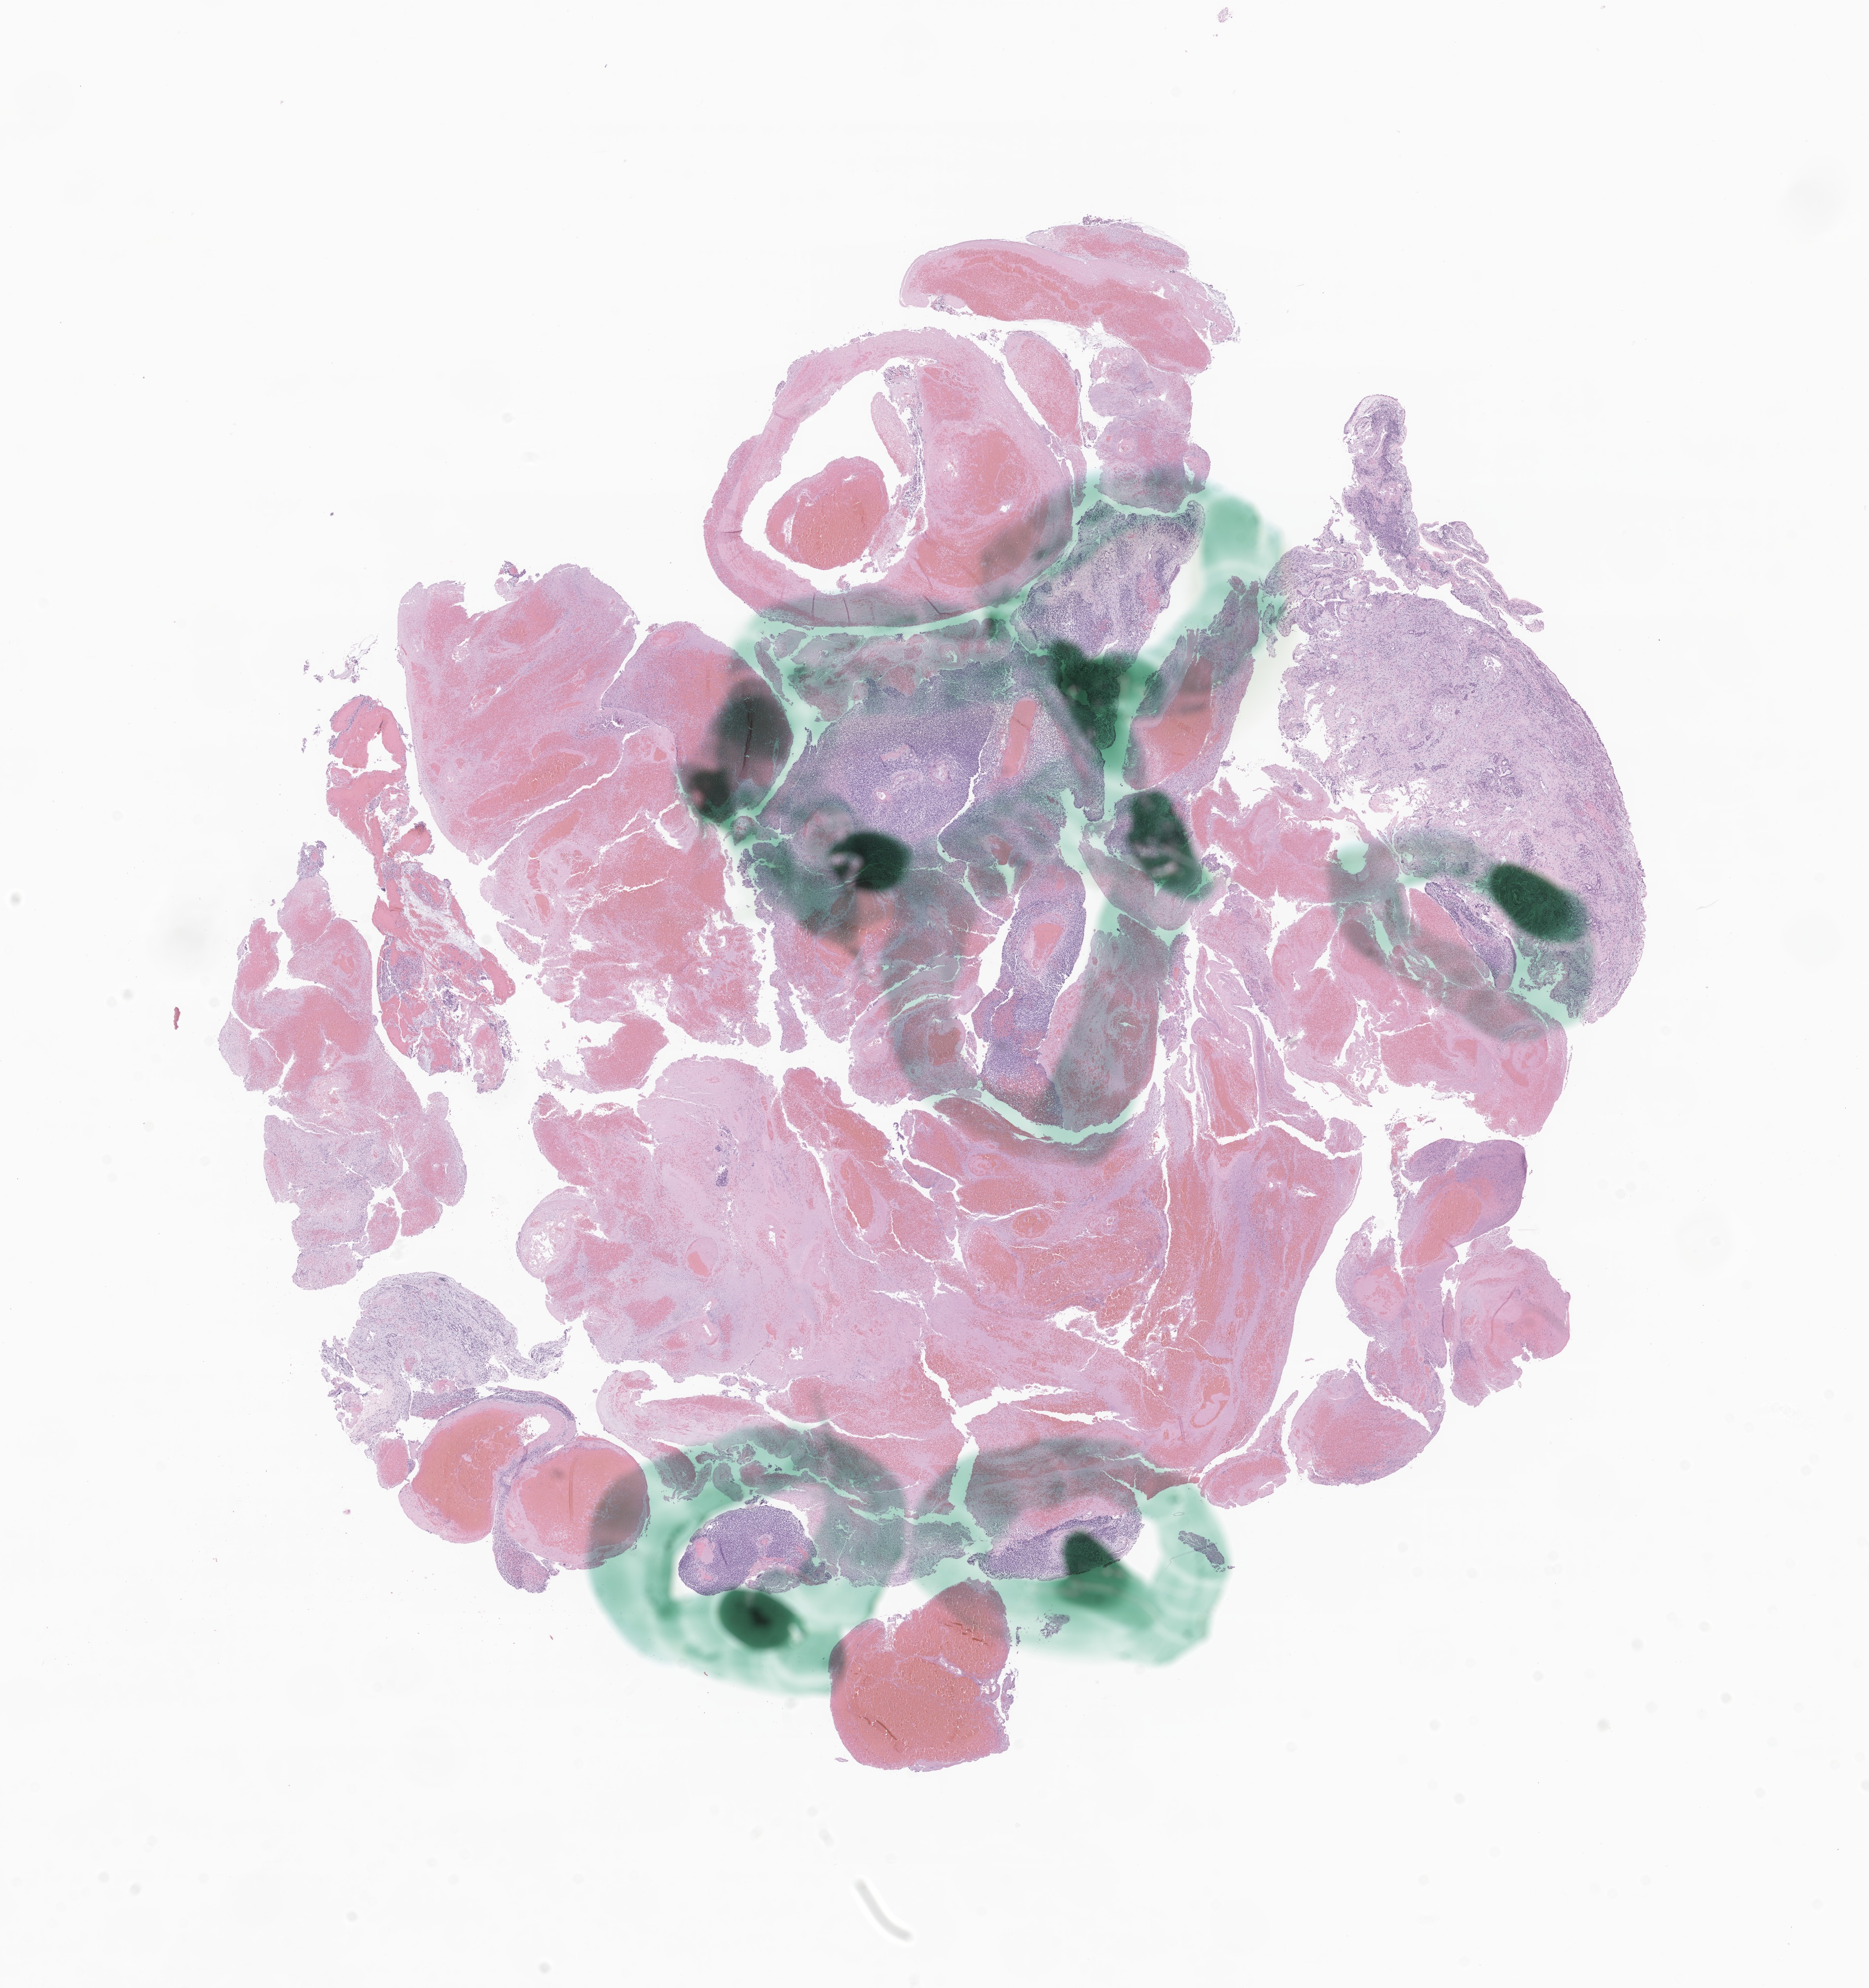
Haematoxylin and eosin whole-slide image of tumor tissue from the nasal cavity — whole scanned area (about 16.0 x 17.0 mm) shown as a low-resolution overview, formalin-fixed paraffin-embedded section. Patient: male, age 89 months (7 years 5 months).
Recorded diagnosis: Embryonal rhabdomyosarcoma, NOS.